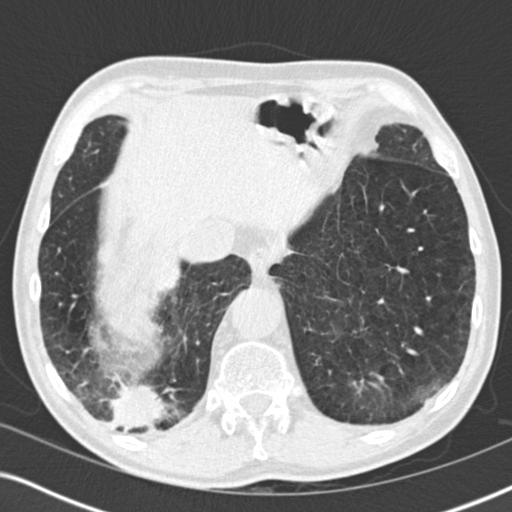
Low-dose screening chest CT, one axial slice. Position 52 of 196 along the scan axis. Reconstruction kernel B30f. Lung window (W 1500 / L -600 HU). 512 × 512 image matrix, field of view 330 × 330 mm.
Annotated regions visible in this slice (outlined manually by an expert reader):
- lesion 3 (tumor, lower lobe of right lung): bounding box [x1, y1, x2, y2] px = [110, 383, 167, 429]